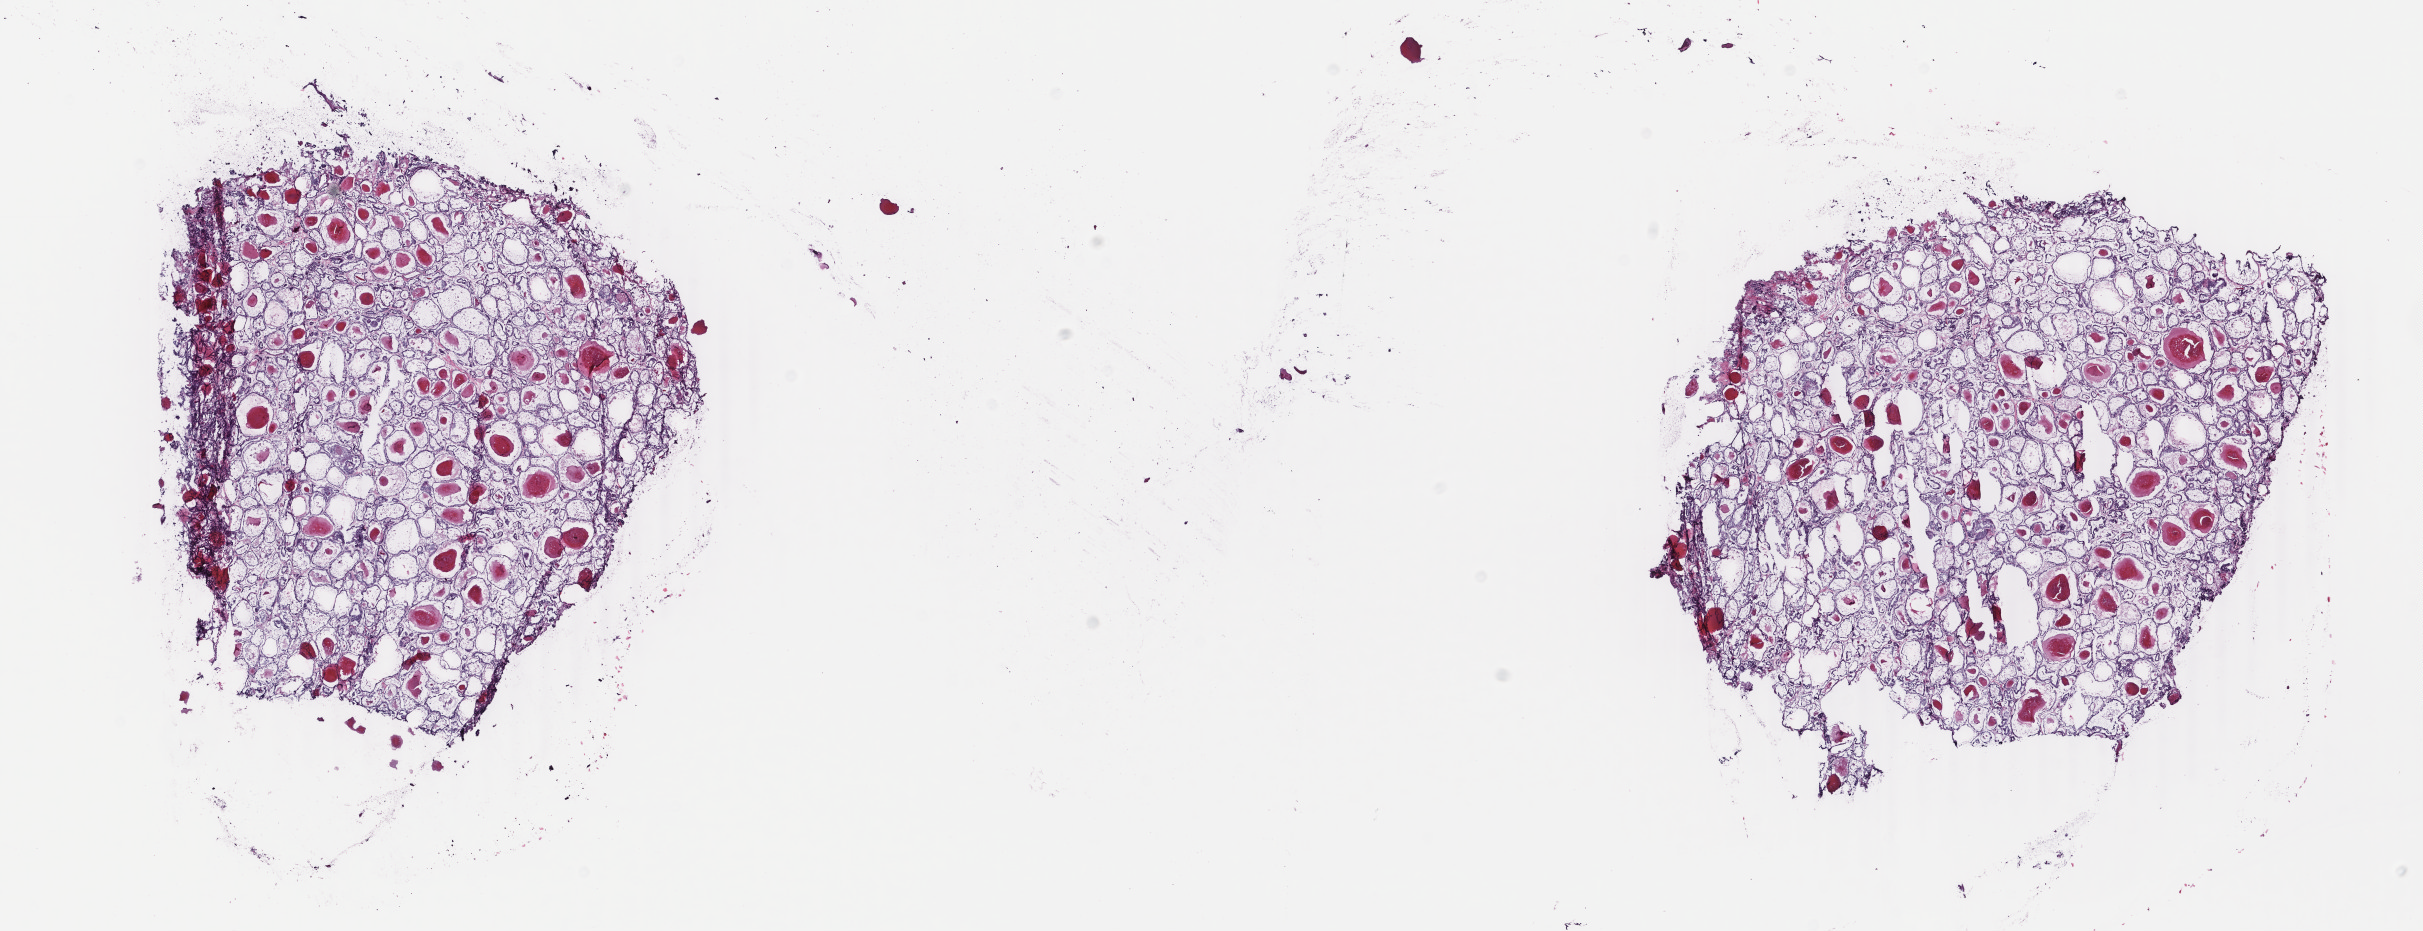
H&E-stained whole-slide image — a low-resolution overview of the entire scanned area, about 19.3 x 7.4 mm (slide scanned at 40x); frozen section; primary tumour sample from the thyroid. Female, age 51 years at initial diagnosis. Slide review estimates, as recorded: tumour cells 100%, tumour nuclei 95%, normal cells 0%, stromal cells 0%, necrosis 0%. Inflammatory infiltration, as recorded: lymphocyte infiltration 0%, monocyte infiltration 0%, neutrophil infiltration 0%.
• diagnosis: Papillary carcinoma, follicular variant
• lymph nodes positive (case pathology): 0 of 1 examined
• AJCC pathologic stage: III (7th edition)